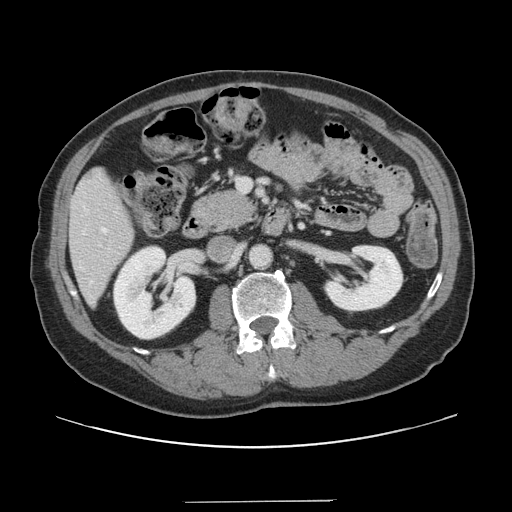
Contrast-enhanced abdominal CT, one axial slice. Slice 57 of 151 in the series (ordered by position). 120 kVp. Intravenous contrast given. Soft-tissue window (W 400 / L 40 HU). 2.5 mm slice thickness. 512 × 512 image matrix, field of view 399 × 399 mm. Male patient, age 63 years. Case-level facts recorded for this patient, not image findings: diagnosis: colorectal cancer liver metastases, imaged before liver resection; multiple liver metastases: no; largest metastasis: 2.1 cm.
Structures marked on this image (expert manual segmentation):
- hepatic veins: bounding box <102,228,107,233> (left, top, right, bottom; pixels)
- liver: <70,170,134,302>
- planned liver remnant (the part of the liver to remain after resection): <70,170,134,302>
- portal vein (with intrahepatic branches): <238,179,251,192>